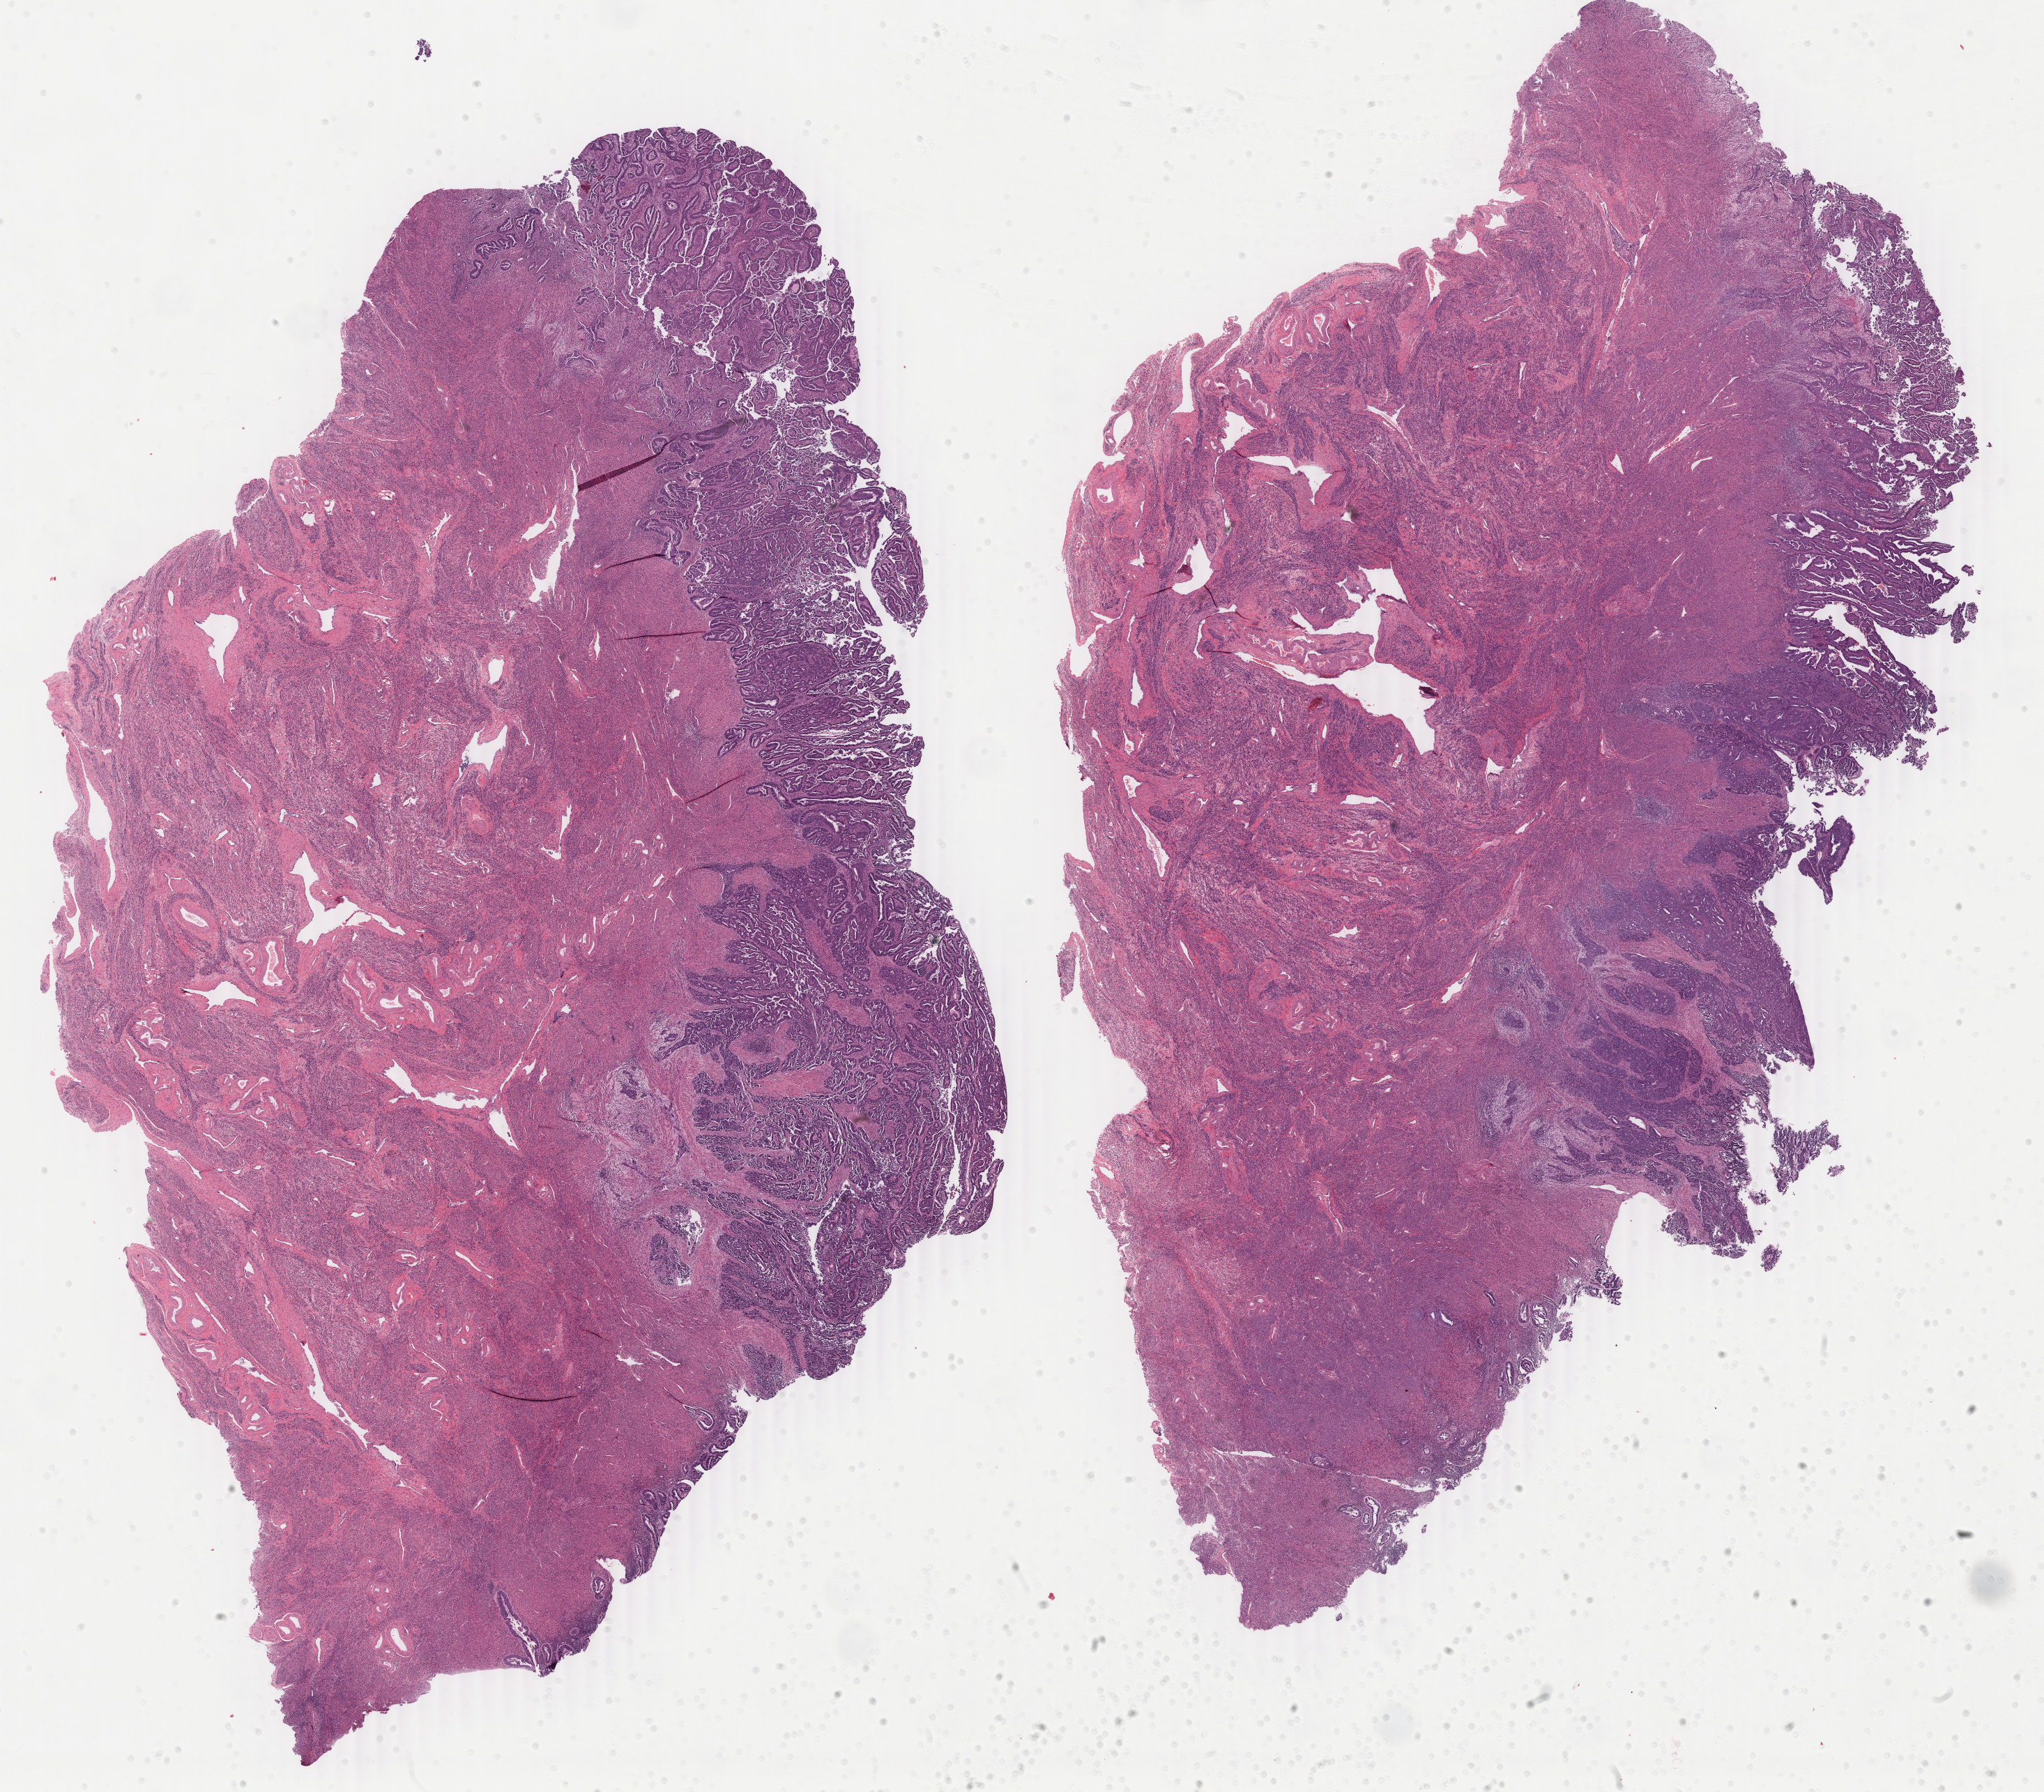
Whole-slide histology image, H&E-stained — shown as a low-resolution overview of the whole scanned area (about 23.3 x 20.4 mm, slide scanned at 40x), formalin-fixed paraffin-embedded (FFPE) diagnostic section, sample: primary tumour, uterus. Patient: female, age at initial diagnosis 59 years. Histologic grade: G3 (poorly differentiated).
• pathologic diagnosis: Serous cystadenocarcinoma, NOS
• FIGO stage: IVA
• lymph nodes positive (case pathology): 0 of 19 examined